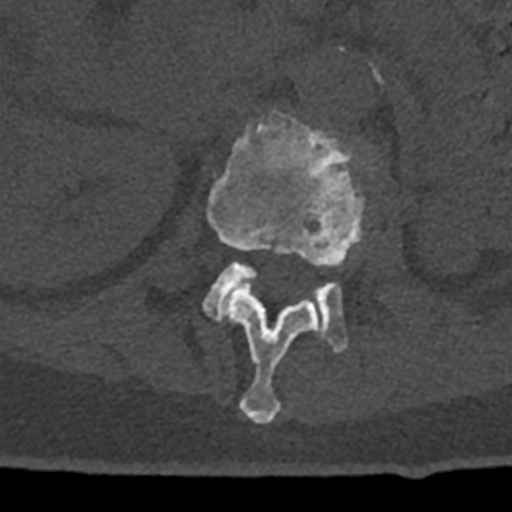
CT including the spine, one axial slice; position 413 of 797 along the scan axis; reconstruction kernel Br40s/3; 120 kVp; bone window (W 1800 / L 400 HU); 512 × 512 image matrix, field of view 160 × 160 mm. Patient: male, 74 years. From the clinical record (not read from this slice): primary cancer: renal.
Outlined on this slice (semi-automatically segmented with operator editing):
- L1 vertebra: box from (x=207, y=110) to (x=364, y=424) px
- L2 vertebra: (x=203, y=261)–(x=349, y=353)